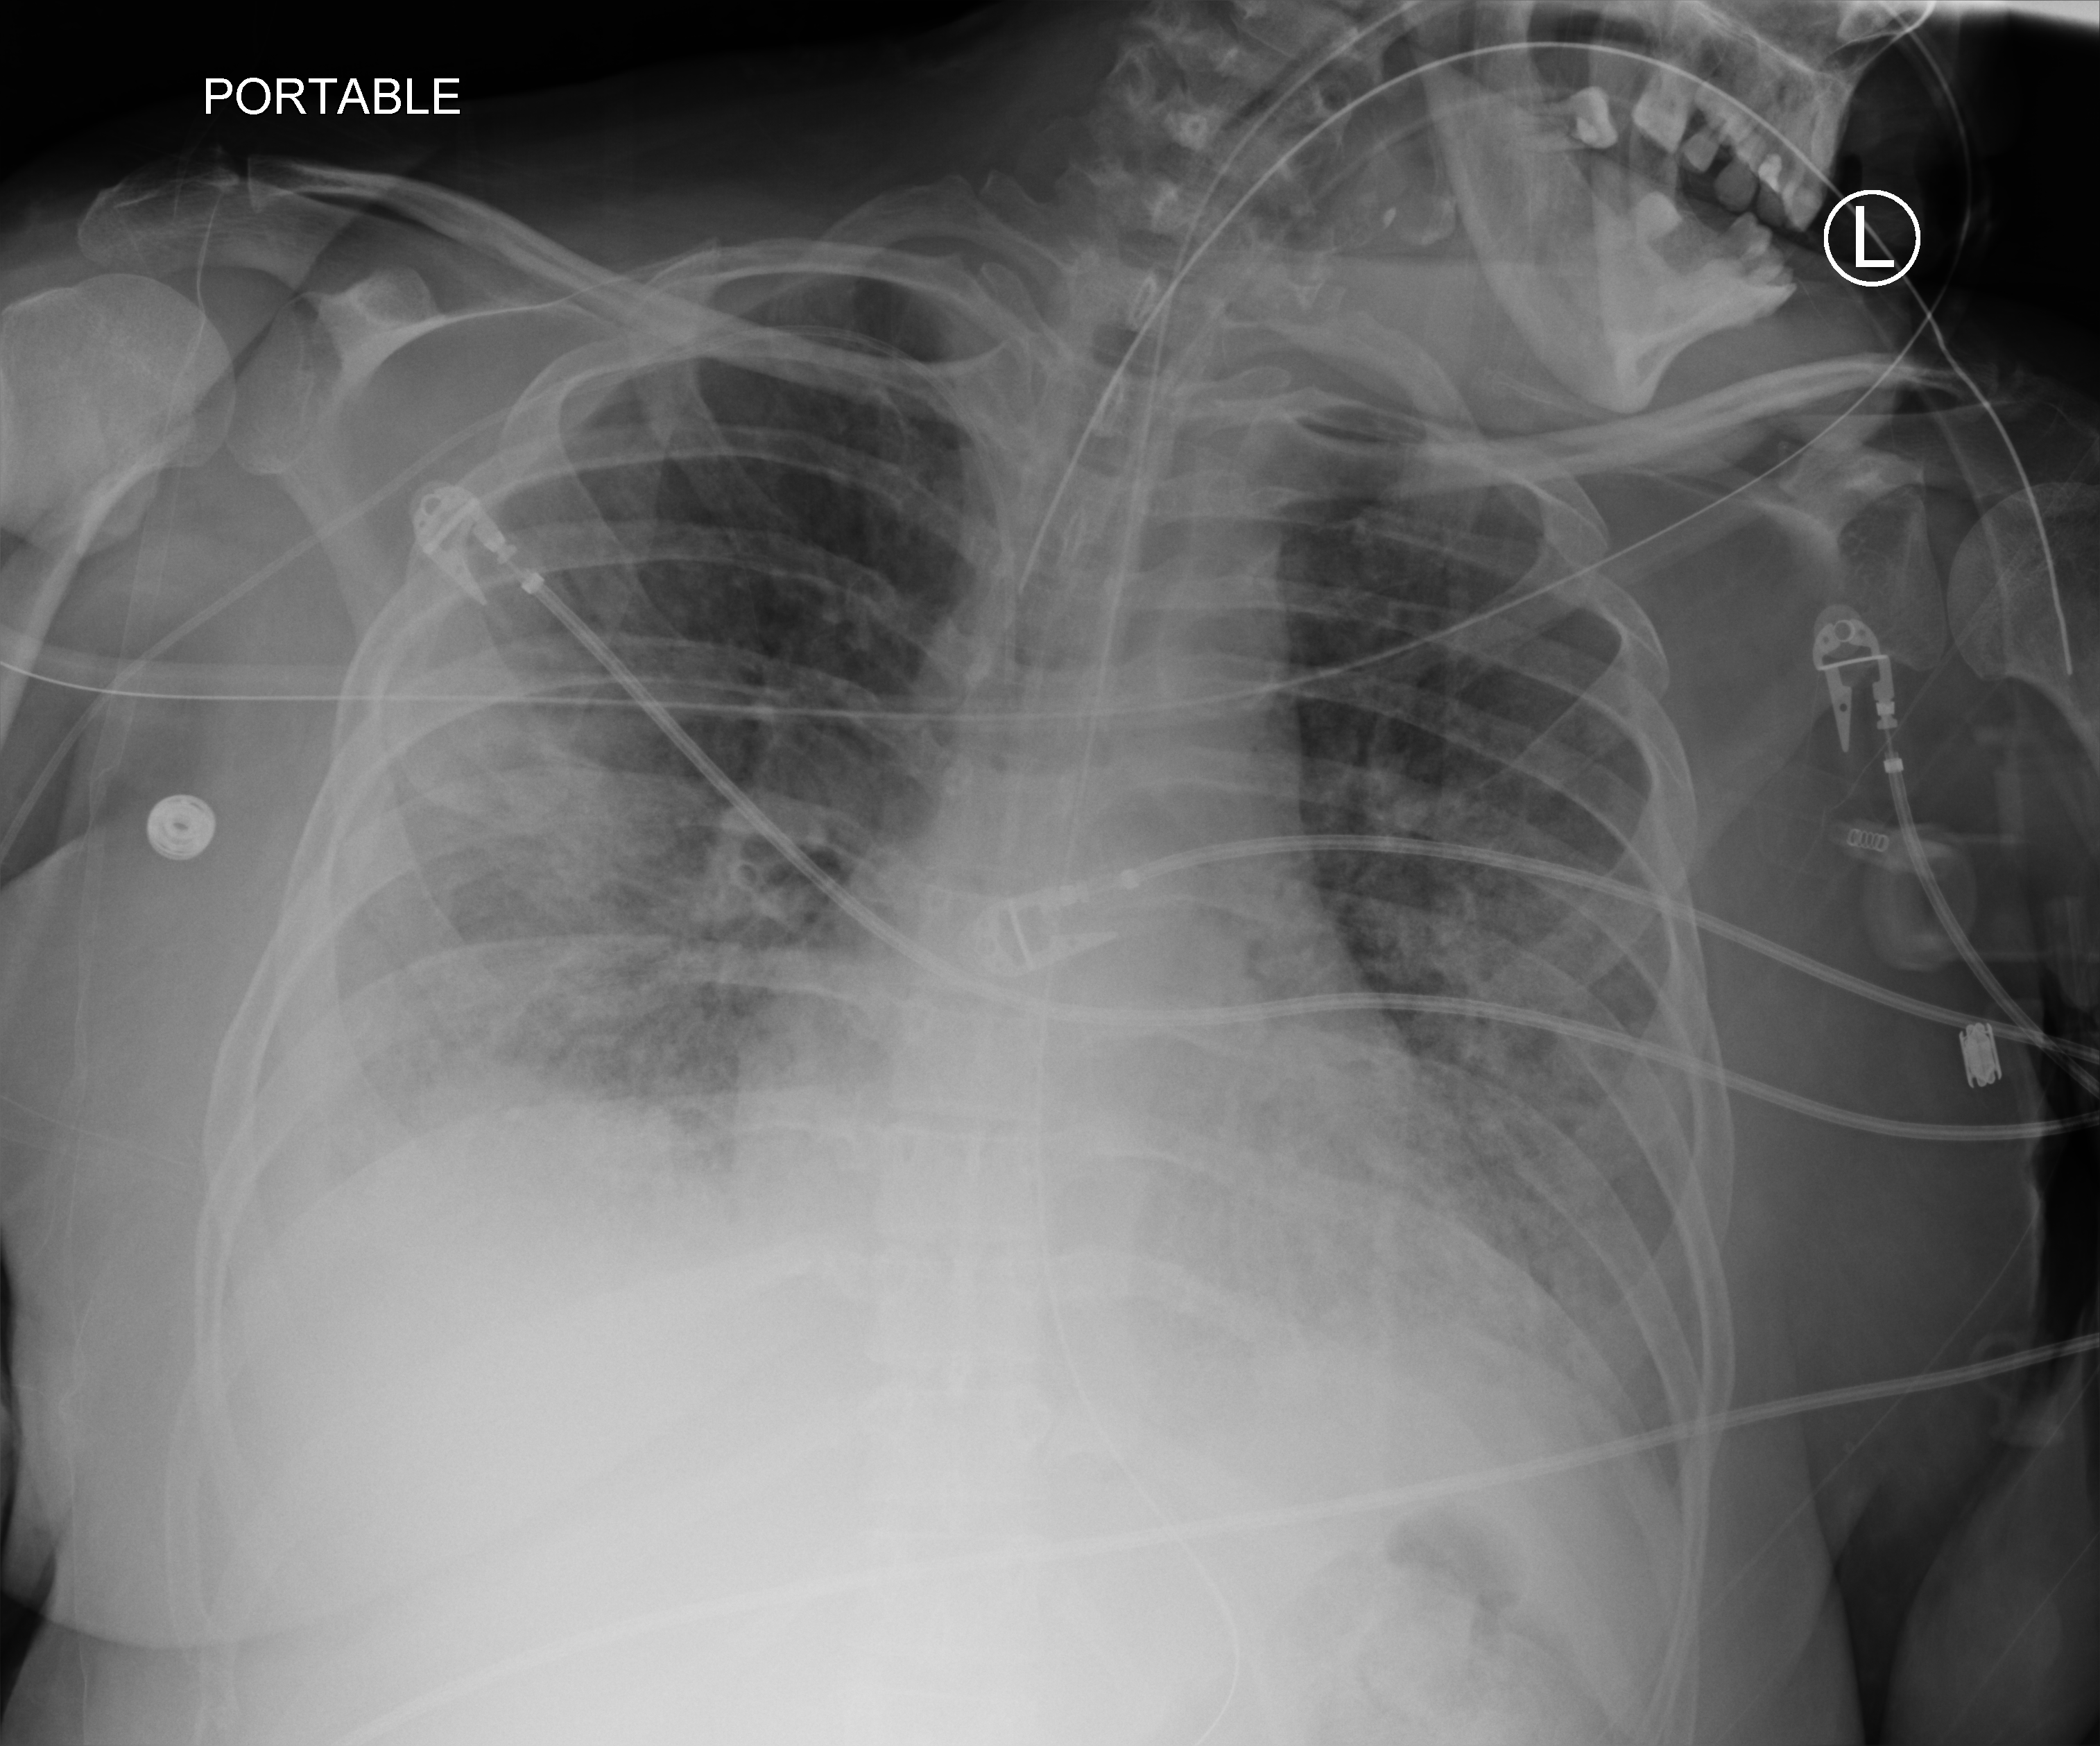
Bedside chest radiograph (computed radiography), anteroposterior (AP) projection. Patient hospitalised with COVID-19, aged 18–59 years.
From the hospital-stay record, not from the radiograph (when in the stay this image was taken is not recorded): admitted to intensive care during this hospital stay: yes.